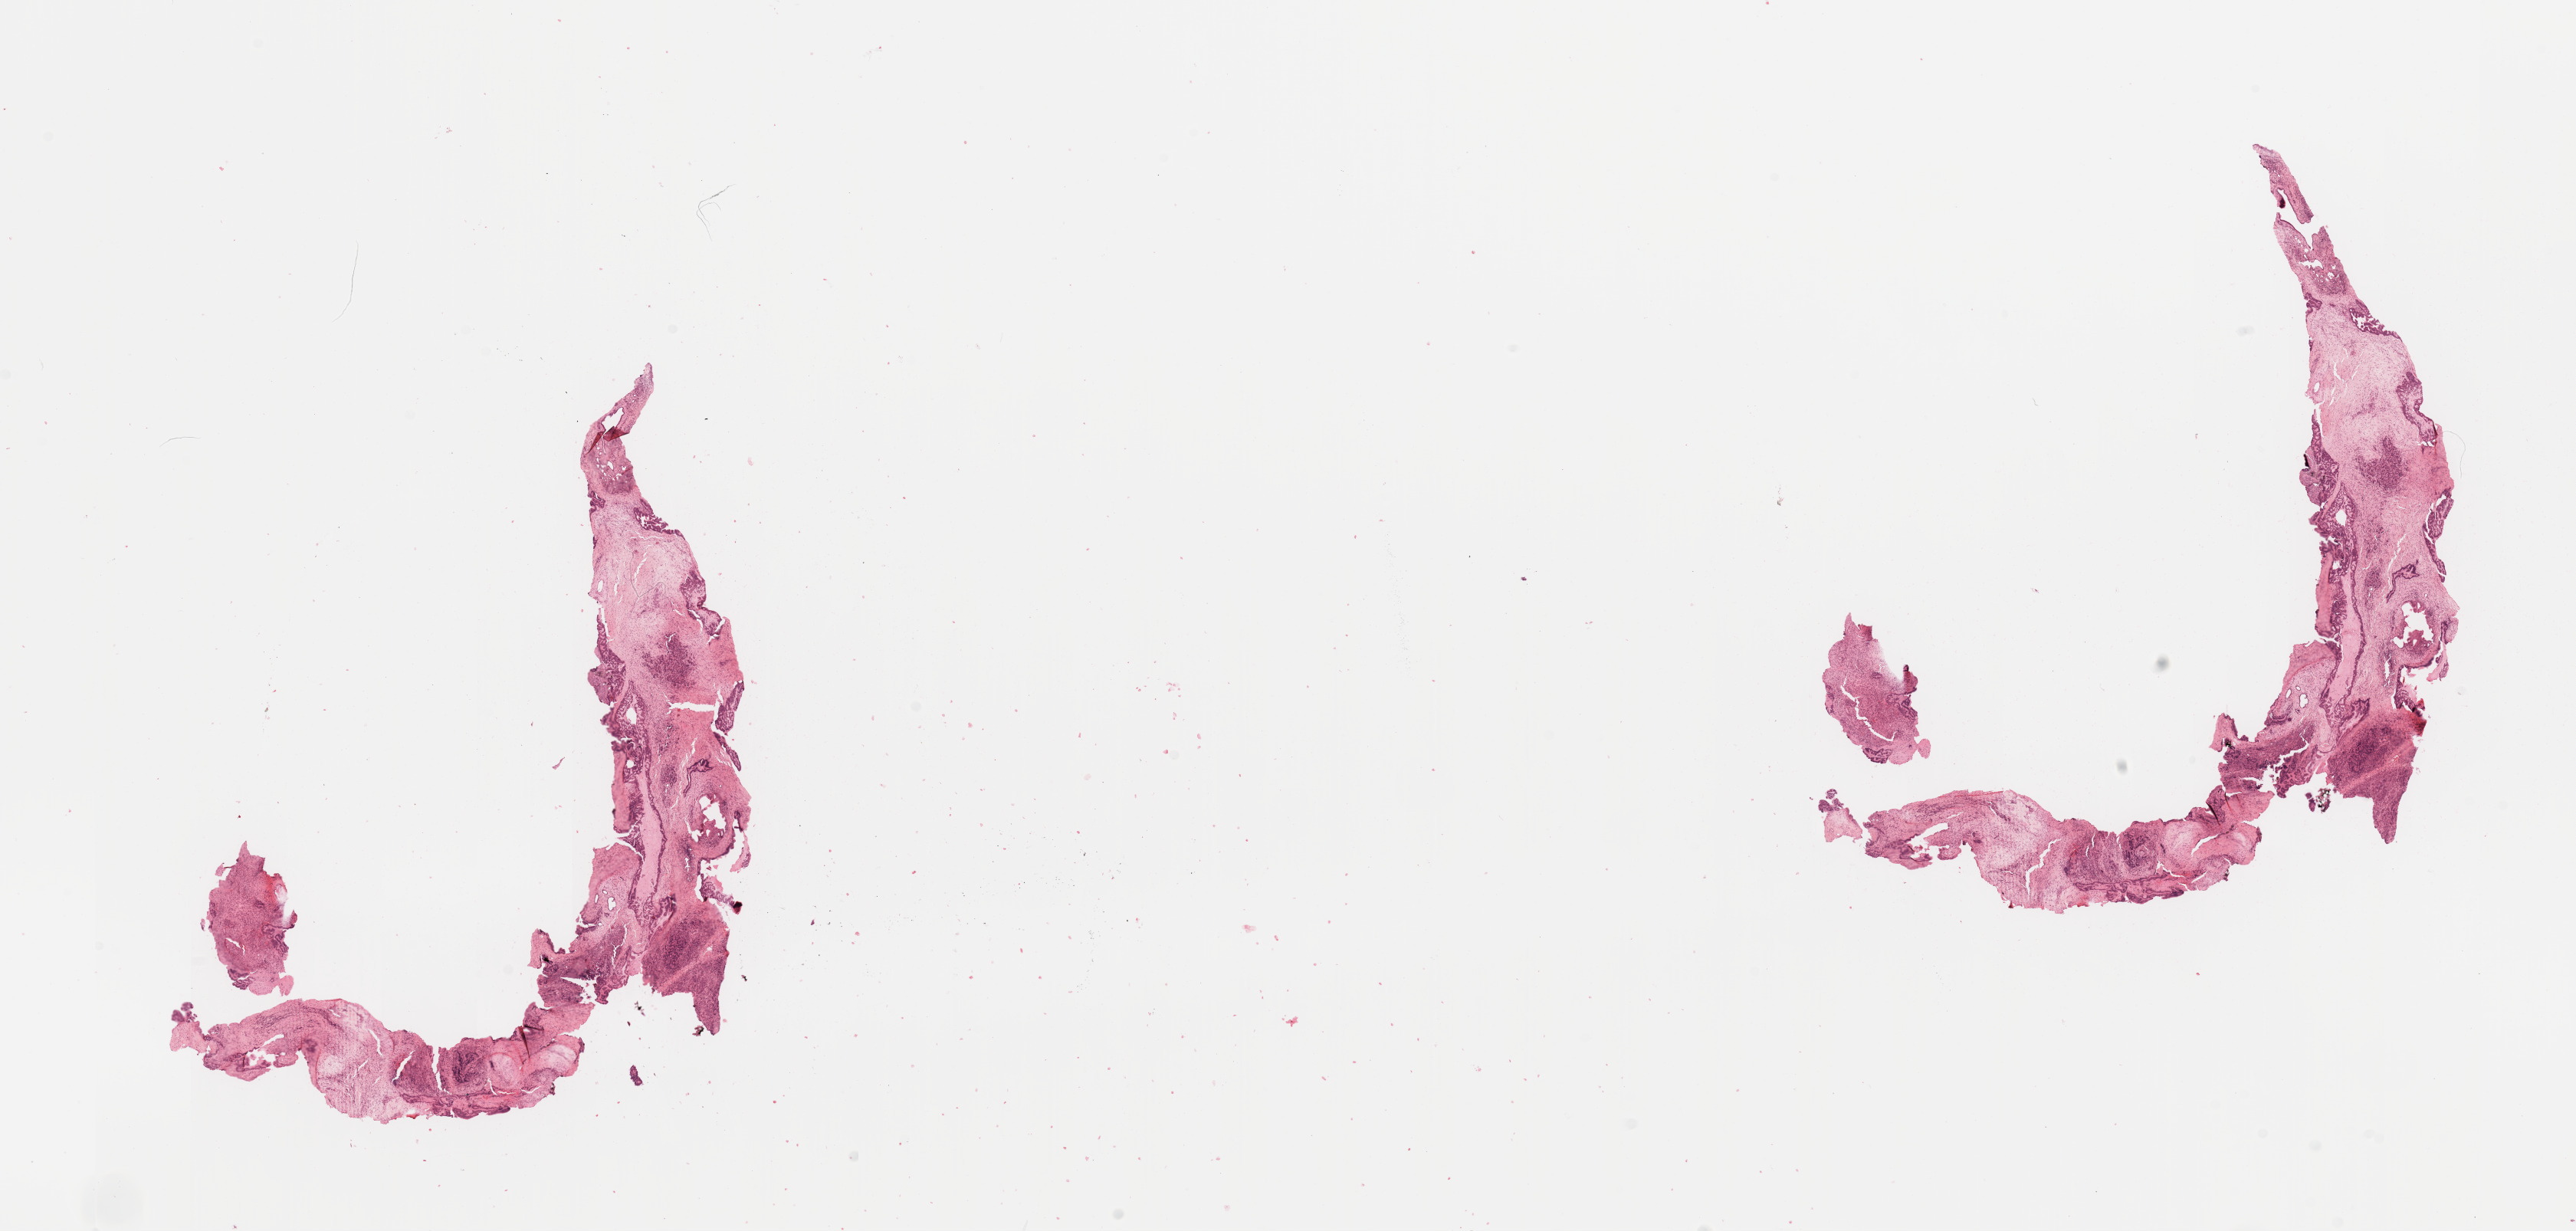
Whole-slide histology image, Hematoxylin and eosin (H&E) stained — whole scanned area (about 26.6 x 12.7 mm, slide scanned at 20x) shown as a low-resolution overview. Tumour tissue sample, sampled site: pancreas. Patient: male, age 64 years. Histologic grade: G2 (moderately differentiated). Composition of this section per pathologist review: tumour nuclei 40%, necrosis 0%.
Diagnosis: Infiltrating duct carcinoma, NOS. AJCC pathologic stage: III. Primary tumour site (as recorded): head.